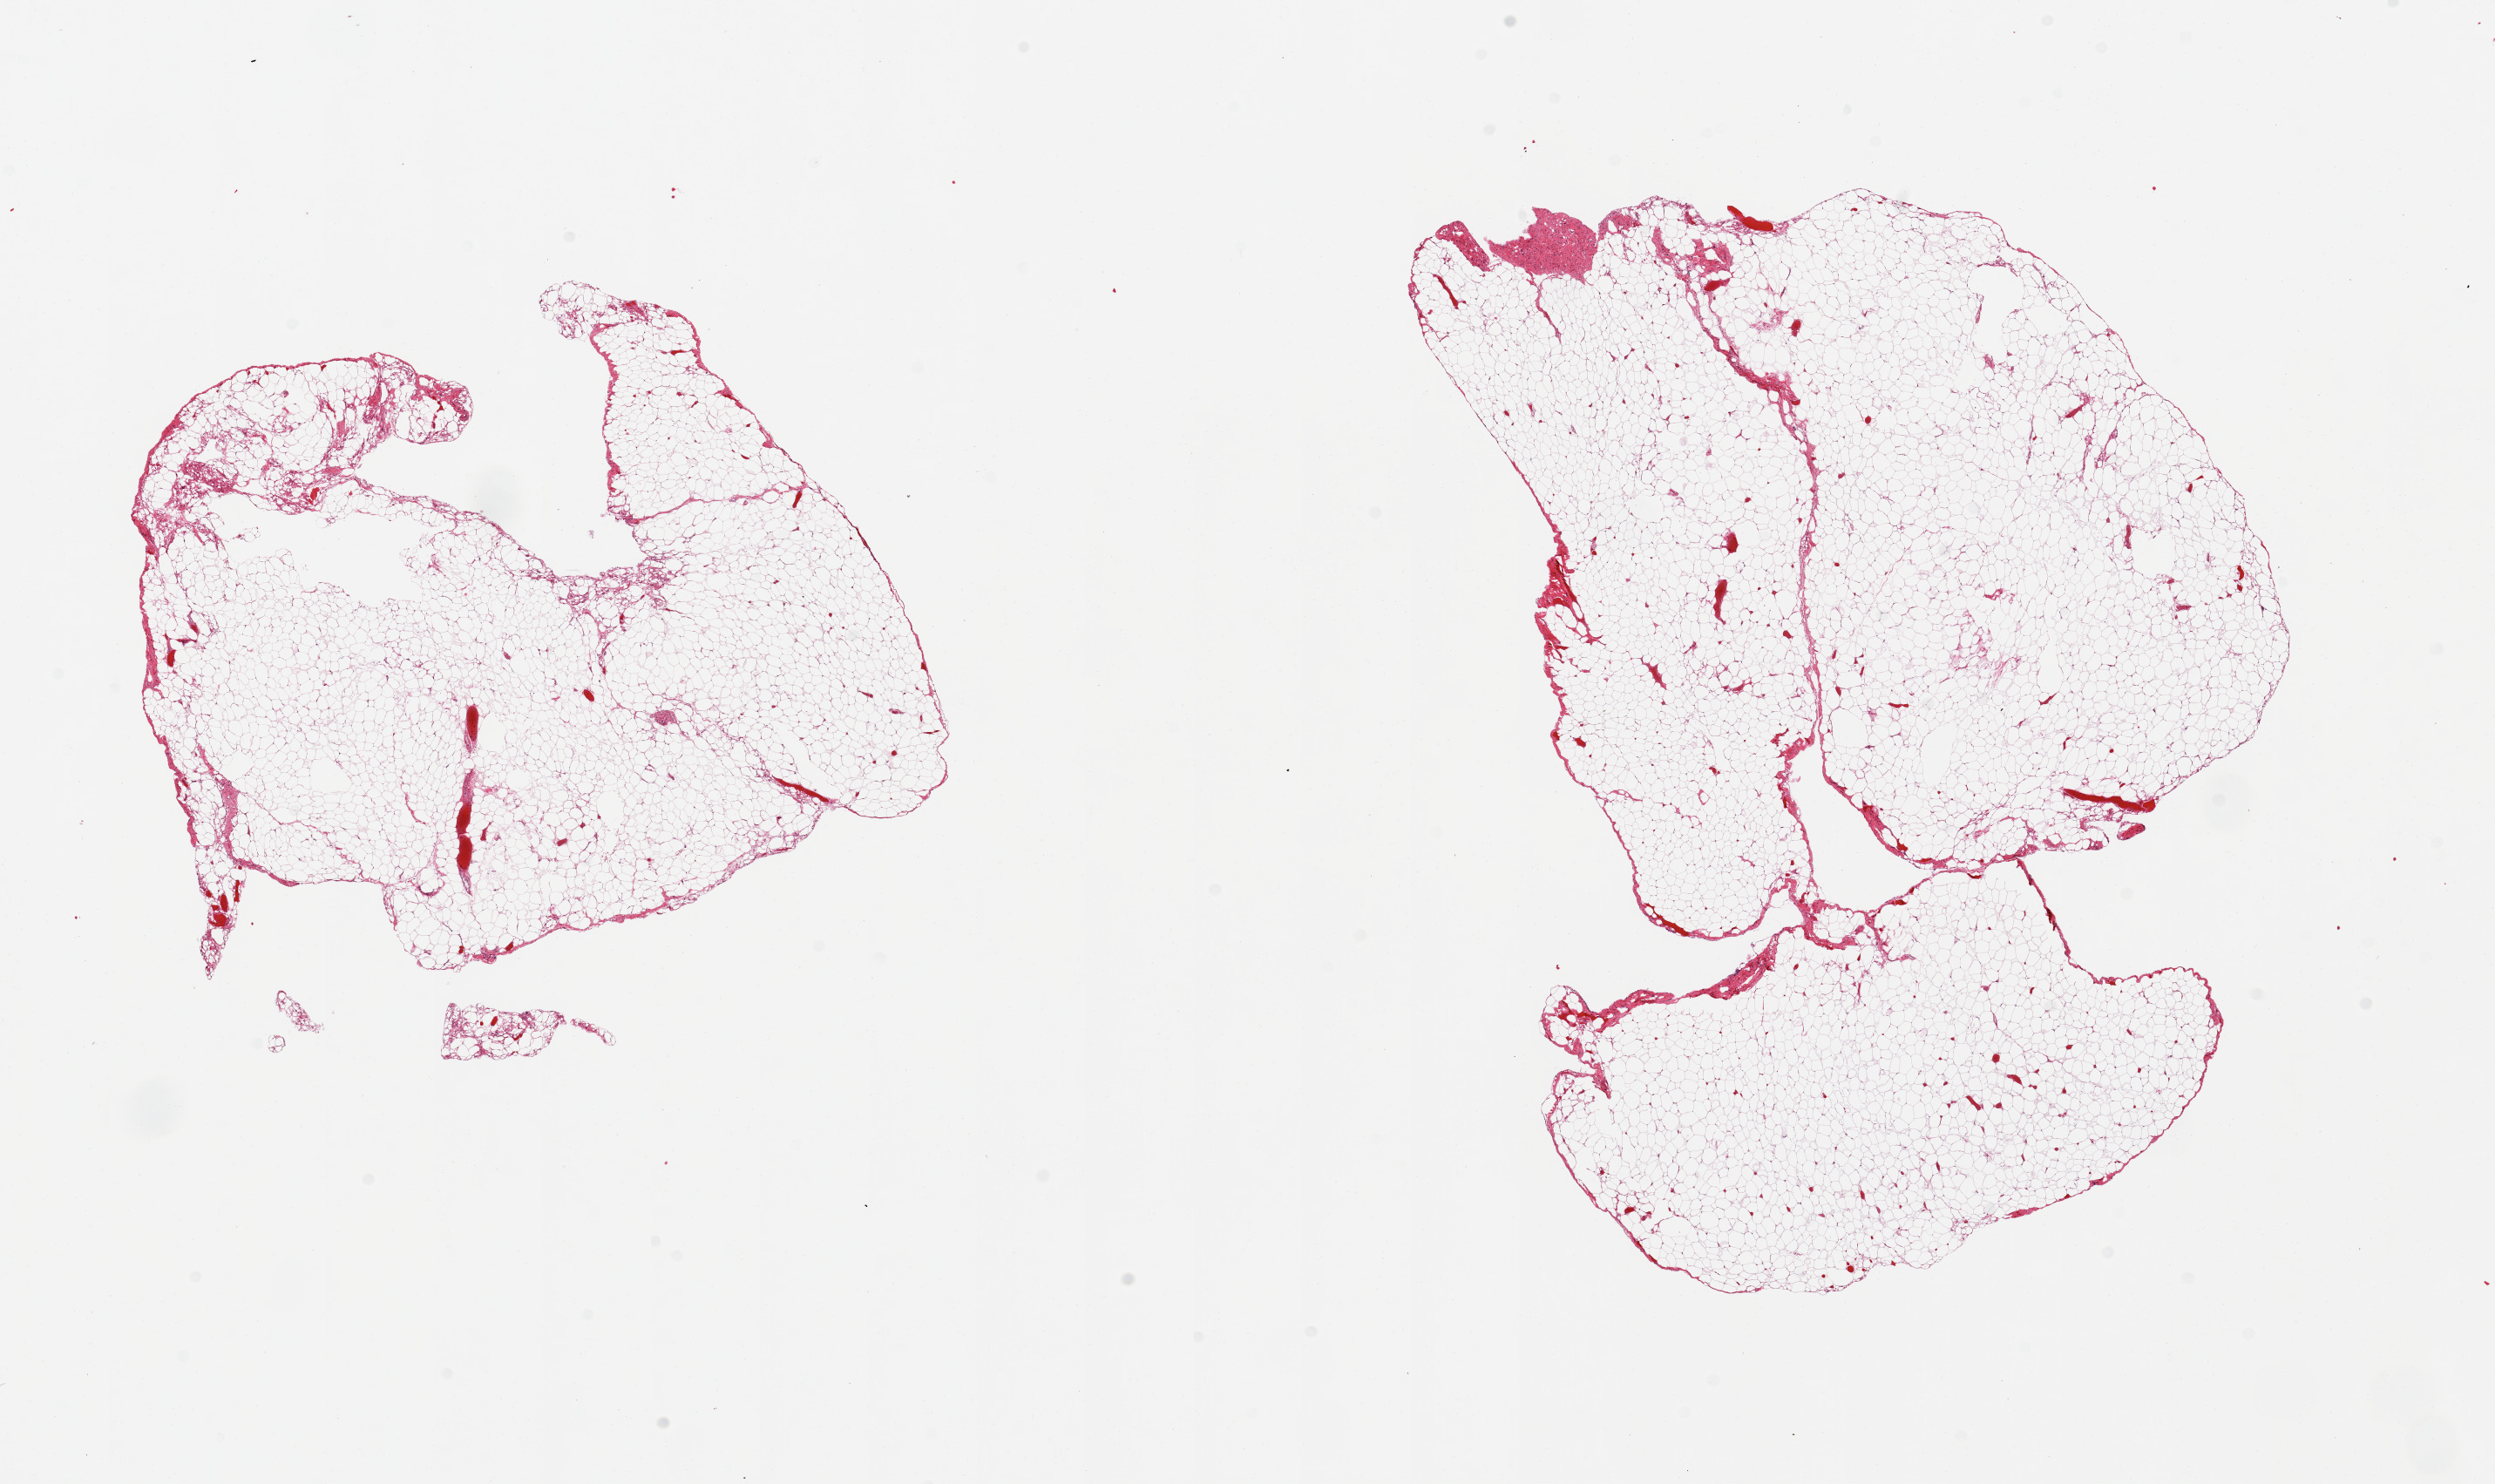
Digitized haematoxylin and eosin-stained section, a low-resolution overview of the entire scanned area, about 22.6 x 13.5 mm (from a 20x scan); PAXgene-fixed, paraffin-embedded tissue; section of omentum (target tissue); tissue donor sample. Male donor.
Pathologist's review note for this sample: 2 pieces, minimal vascular fibrous tissue.